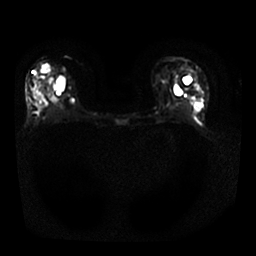
Breast MRI, one axial slice. Position 16 of 25 along the scan axis. Diffusion-weighted series; image 2 of 4 stored at this slice position (different b-values; order by instance number). 1.5 T. 4 mm slice thickness. 256 × 256 image matrix, field of view 330 × 330 mm. Female patient.
Outlined on this slice (outlined manually by an expert reader):
- tumour on diffusion-weighted imaging: box from (x=31, y=75) to (x=55, y=108) px